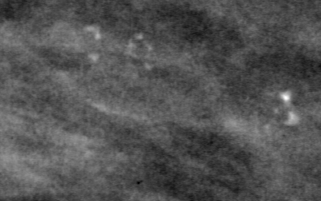
Region of interest cut from a scanned film mammogram (one marked finding), right breast, MLO view.
Calcifications, morphology pleomorphic, distribution clustered; BI-RADS assessment category 4; pathology (as recorded): benign.